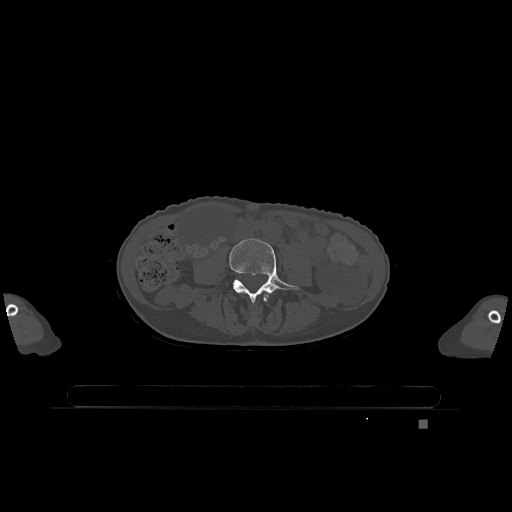
CT including the spine, one axial slice. Position 300 of 1317 along the scan axis. Bone window (W 1800 / L 400 HU). 512 × 512 image matrix, field of view 500 × 500 mm. Patient: female, 74 years. From the clinical record (not read from this slice): primary cancer: lung; vertebrae with lytic lesions (as recorded): T1, T4, T5, T6, L4, L5.
Outlined on this slice (semi-automatic segmentation, software-assisted and operator-edited):
- L3 vertebra: box from (x=263, y=293) to (x=270, y=302) px
- L4 vertebra: (x=230, y=239)–(x=300, y=303)